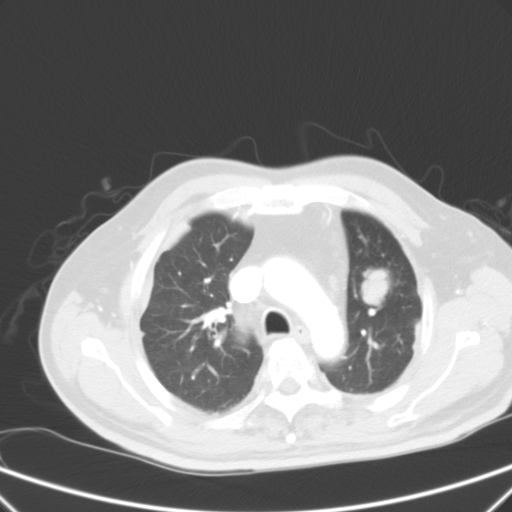
Chest CT, one axial slice. Slice 43 of 59 in the series (ordered by position). Lung window (W 1500 / L -600 HU). 512 × 512 image matrix. Patient: male, 66 years. From the clinical record (not read from this slice): clinical TNM (as recorded): T1c N3 M1a.
Structures marked on this image (bounding box drawn by a radiologist):
- lung tumour (recorded histology: squamous cell carcinoma): box from (x=355, y=264) to (x=397, y=315) px